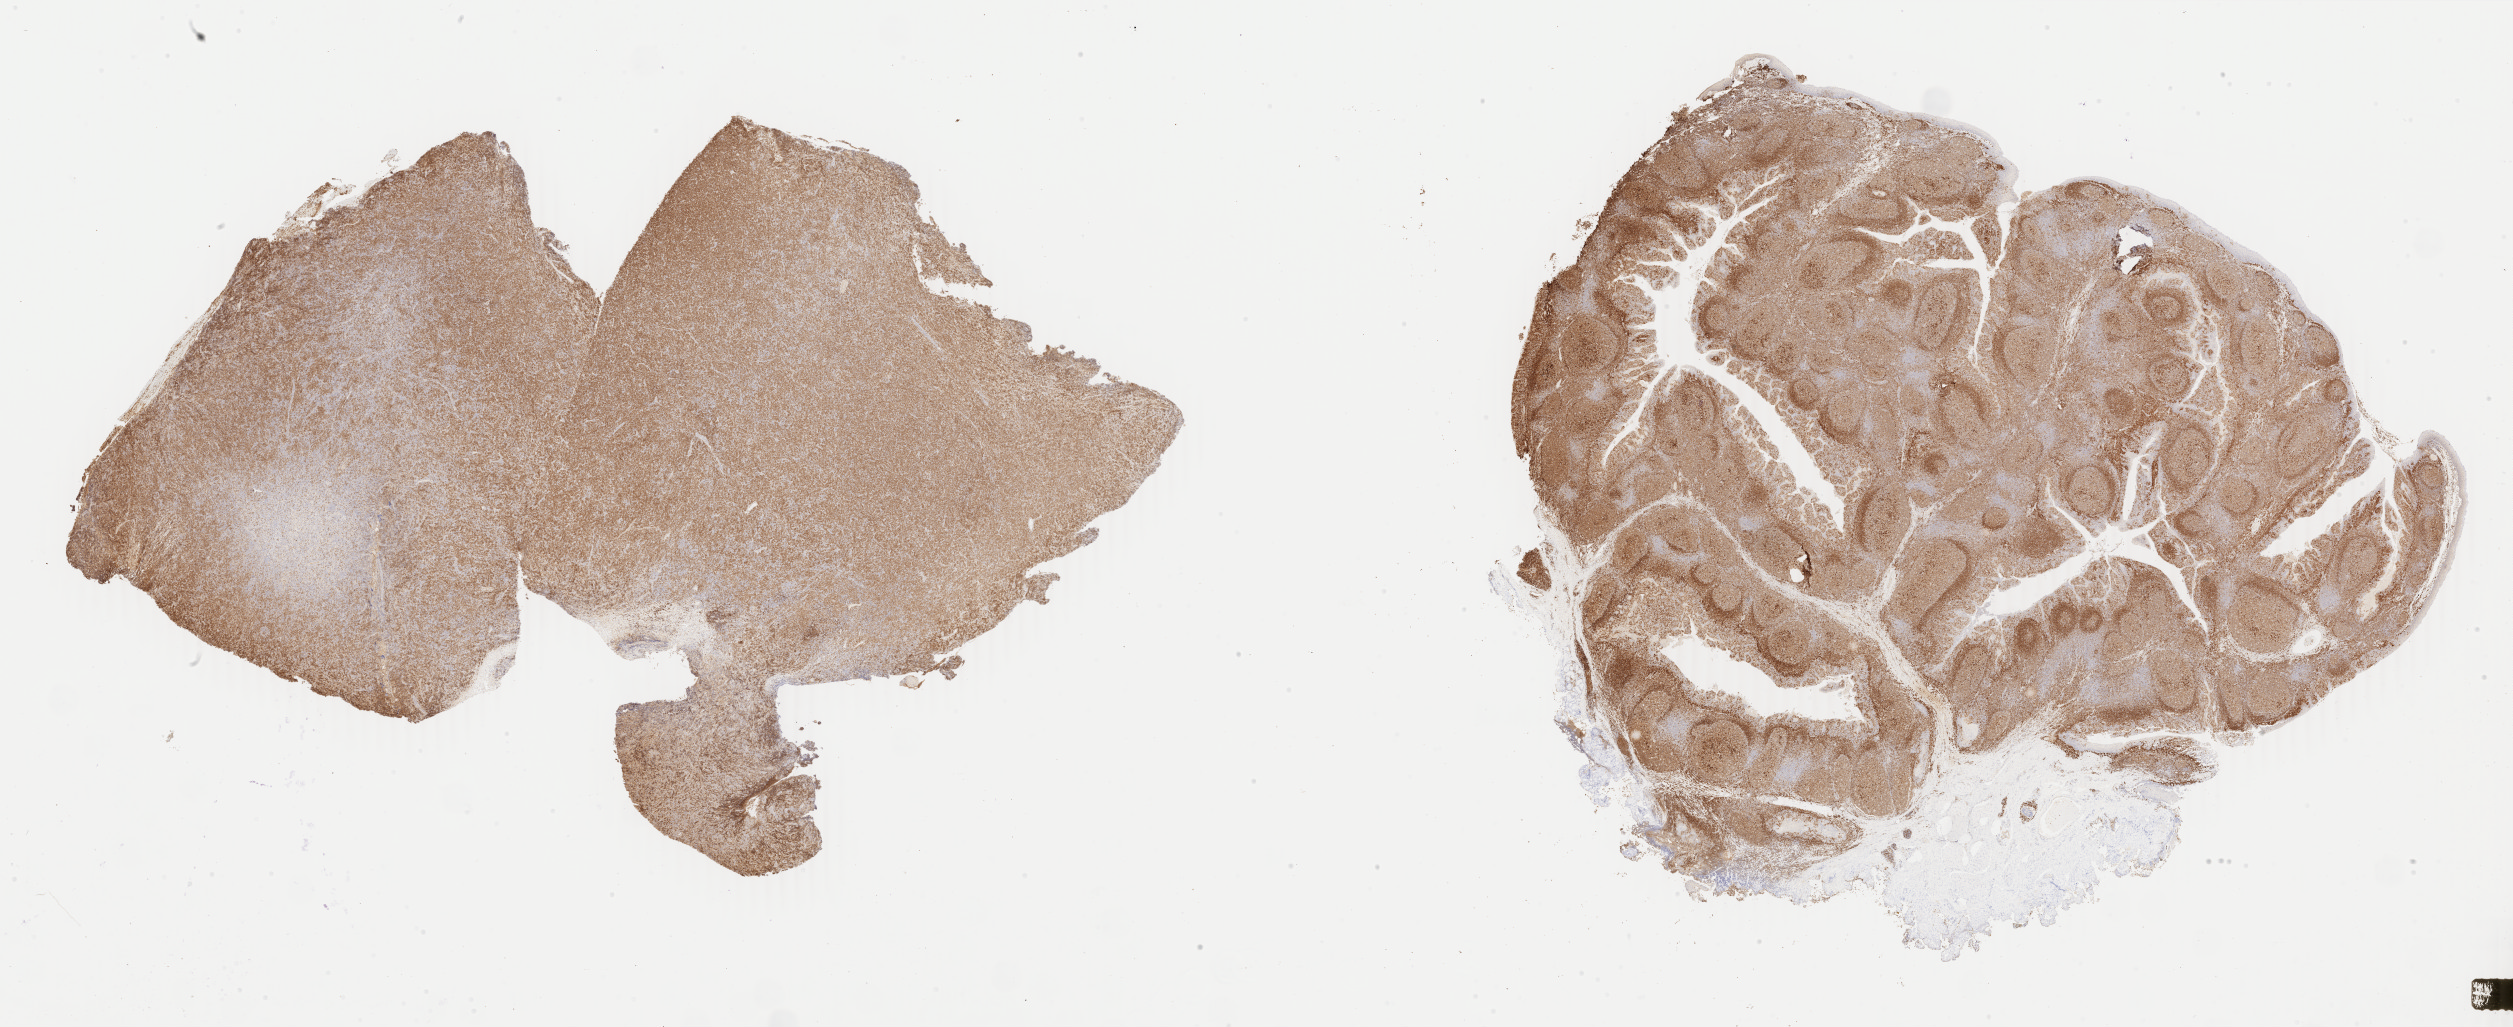
IHC for CD79a, whole-slide image, whole scanned area (about 40.0 x 16.3 mm) shown as a low-resolution overview. Tumor tissue. Patient: male, age at initial diagnosis 7 years.
Histologic diagnosis: Diffuse large B-cell lymphoma, NOS.